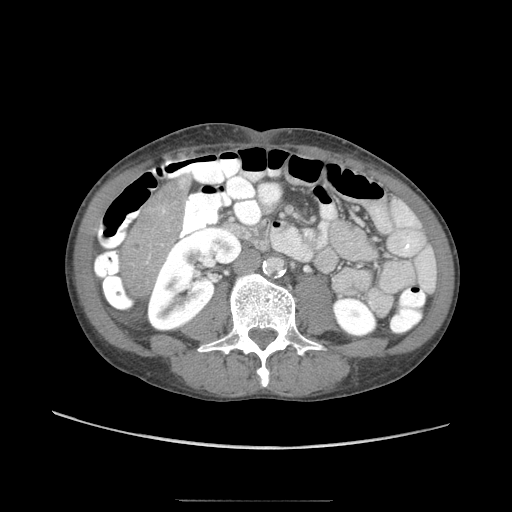
Contrast-enhanced abdominal CT (liver protocol), one axial slice; 120 kVp; soft-tissue window (W 400 / L 40 HU); 2.5 mm slice thickness; 512 × 512 image matrix, field of view 380 × 380 mm. From the clinical record (not read from this slice): diagnosis: hepatocellular carcinoma (patient treated with transarterial chemoembolisation; whether this scan precedes or follows treatment is not stated here); TNM stage (as recorded): Stage-IIIA; Child-Pugh class: A; tumour differentiation: moderately differentiated; tumour nodularity: multinodular.
Outlined on this slice (semi-automatic segmentation, software-assisted and operator-edited):
- liver parenchyma outside the tumour (the mass and vessels are separate outlines, so this box may not span the whole liver): bounding box <120,175,190,302> (left, top, right, bottom; pixels)